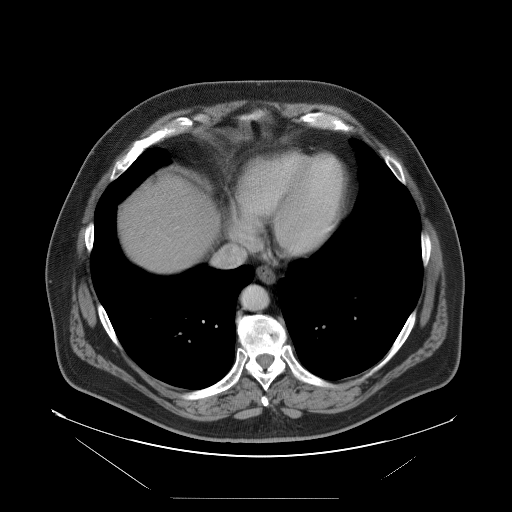
Contrast-enhanced abdominal CT, one axial slice. Slice 94 of 114 in the series (ordered by position). 120 kVp. Intravenous contrast given. Soft-tissue window (W 400 / L 40 HU). 5 mm slice thickness. 512 × 512 image matrix, field of view 500 × 500 mm. Male patient, age 61 years. From the clinical record (not read from this slice): diagnosis: colorectal cancer liver metastases, imaged before liver resection; multiple liver metastases: no; largest metastasis: 6.5 cm; disease in both lobes: yes.
Annotated regions visible in this slice (expert manual segmentation):
- hepatic veins: box from (x=214, y=214) to (x=253, y=267) px
- liver: (x=119, y=178)–(x=215, y=272)
- planned liver remnant (the part of the liver to remain after resection): (x=165, y=178)–(x=219, y=244)